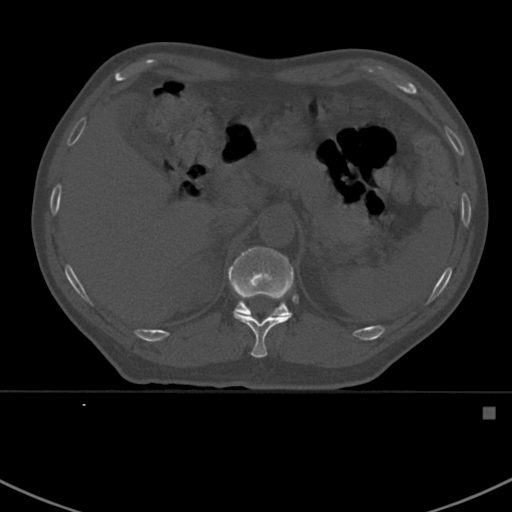
CT including the spine, one axial slice; position 340 of 412 along the scan axis; reconstruction kernel Br40s; bone window (W 1800 / L 400 HU); 1.5 mm slice thickness; 512 × 512 image matrix. Male patient, age 59 years. From the clinical record (not read from this slice): primary cancer: prostate.
Outlined on this slice (semi-automatically segmented with operator editing):
- T11 vertebra: box from (x=234, y=313) to (x=292, y=358) px
- T12 vertebra: (x=228, y=246)–(x=294, y=316)